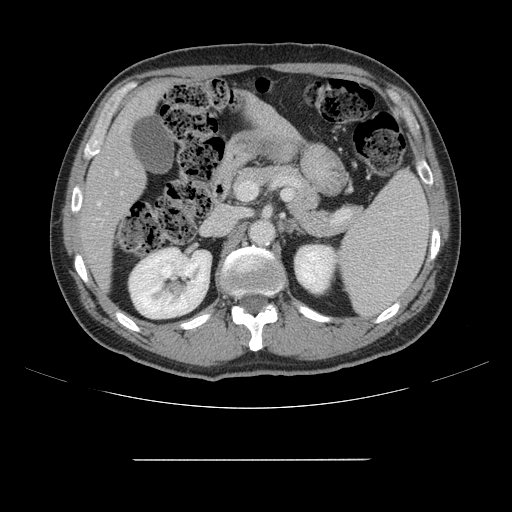
Contrast-enhanced abdominal CT, one axial slice; slice 79 of 164 in the series (ordered by position); intravenous contrast given; soft-tissue window (W 400 / L 40 HU); 2.5 mm slice thickness; 512 × 512 image matrix, field of view 404 × 404 mm. Male patient, age 54 years. From the clinical record (not read from this slice): diagnosis: colorectal cancer liver metastases, imaged before liver resection; multiple liver metastases: yes; largest metastasis: 1 cm; disease in both lobes: no.
Structures marked on this image (expert manual segmentation):
- hepatic veins: bounding box (x1, y1, x2, y2) in pixels: (97, 171, 118, 206)
- liver: (83, 88, 291, 285)
- planned liver remnant (the part of the liver to remain after resection): (83, 88, 160, 284)